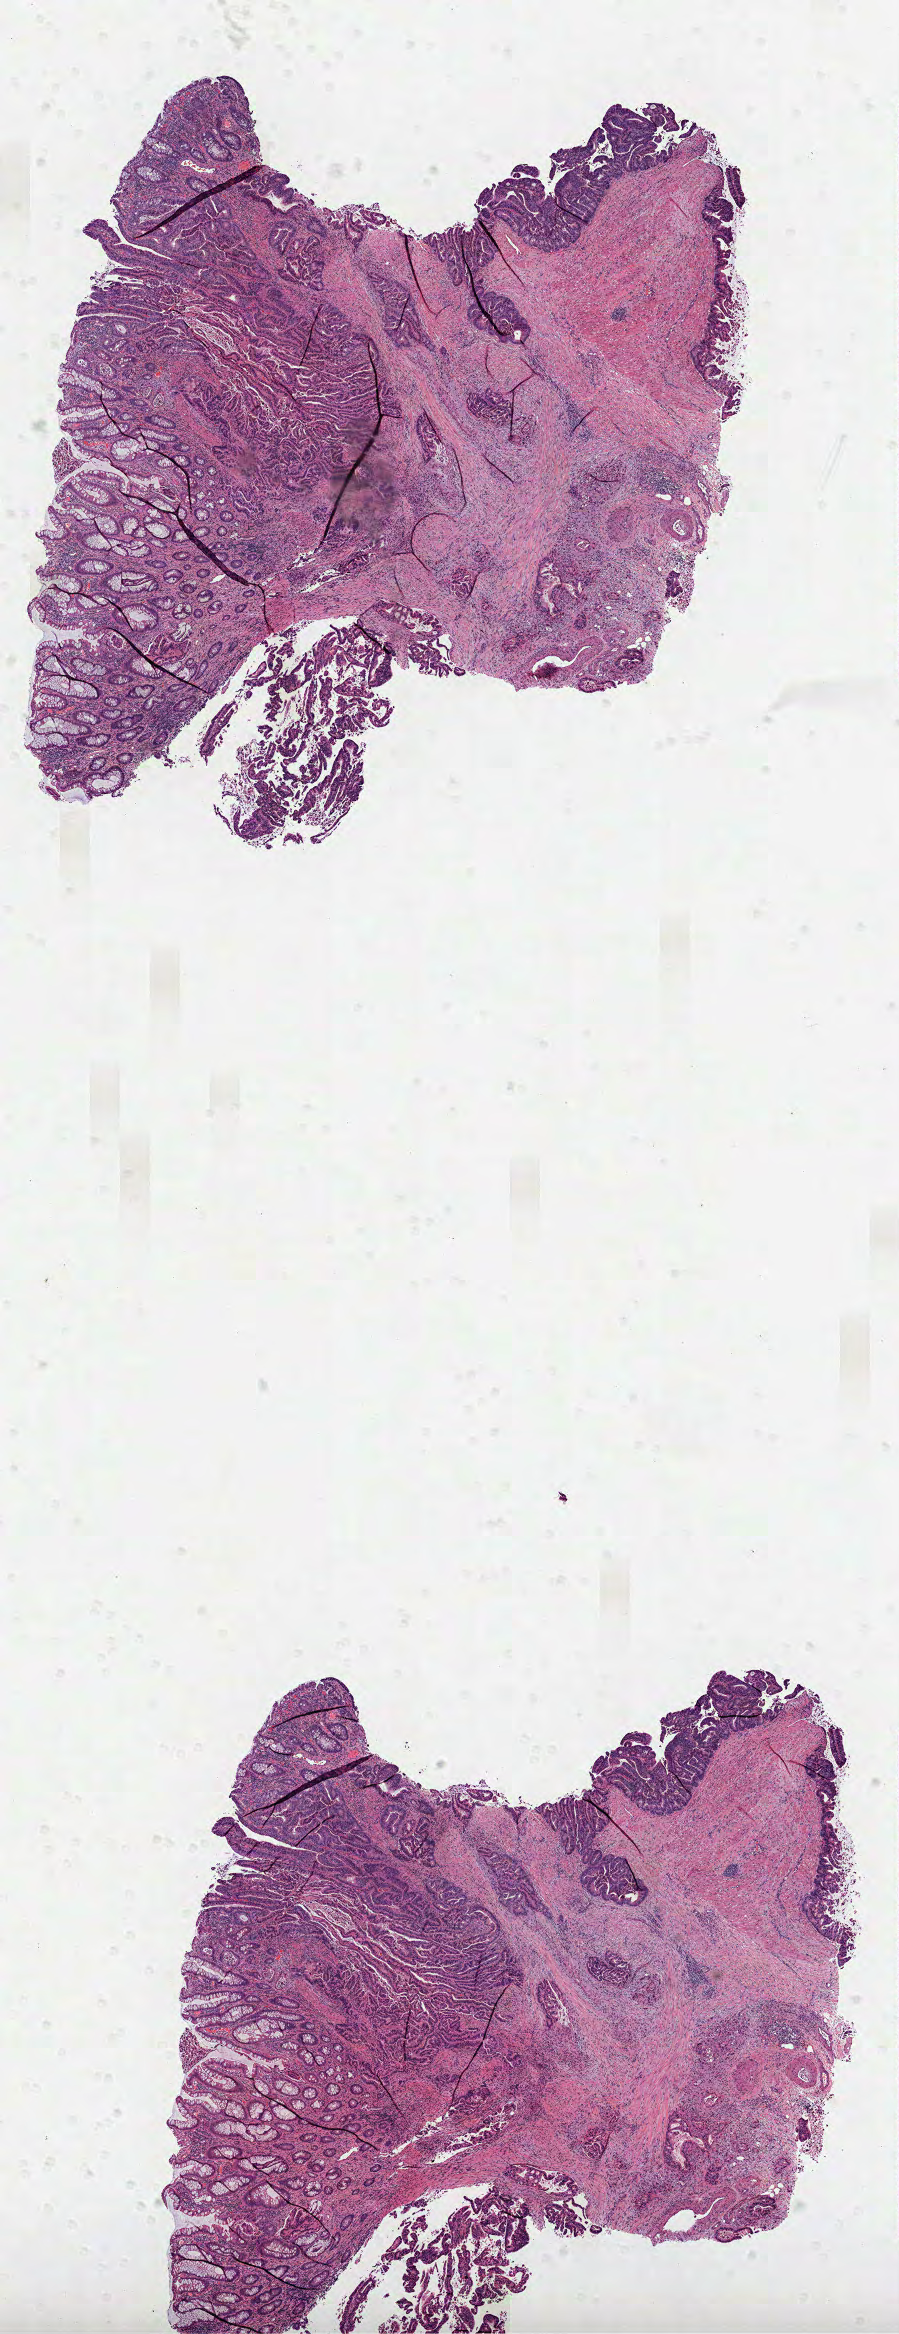
H&E-stained whole-slide image, a low-resolution overview of the entire scanned area, about 7.3 x 18.8 mm (acquisition: 40x scan); formalin-fixed paraffin-embedded (FFPE) diagnostic section; colon, primary tumour sample. Male patient; age at initial diagnosis 66 years.
* AJCC pathologic stage: IIIB
* lymph nodes positive (case pathology): 2 of 23 examined
* diagnosis: Adenocarcinoma, NOS